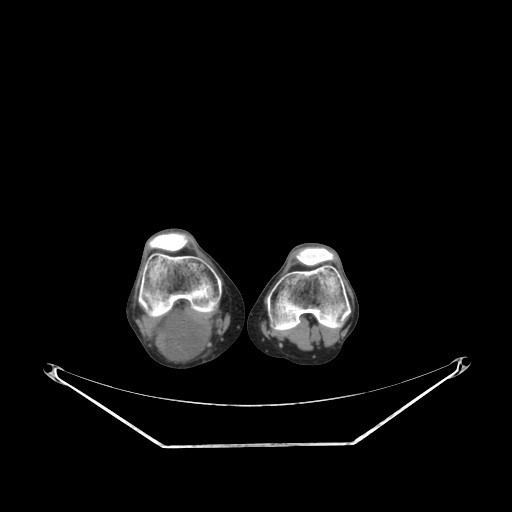
CT of an extremity soft-tissue mass (from a PET/CT study), one axial slice. Position 169 of 267 along the scan axis. Reconstruction kernel SOFT. Soft-tissue window (W 400 / L 40 HU). 3.75 mm slice thickness. 512 × 512 image matrix, field of view 500 × 500 mm. Female patient. From the clinical record (not read from this slice): histological type: liposarcoma; site of the primary tumour: right thigh.
Structures marked on this image (expert contour drawn on MRI and transferred to this co-registered scan by the dataset authors):
- gross tumour volume (mass): bounding box <153,306,211,362> (left, top, right, bottom; pixels)